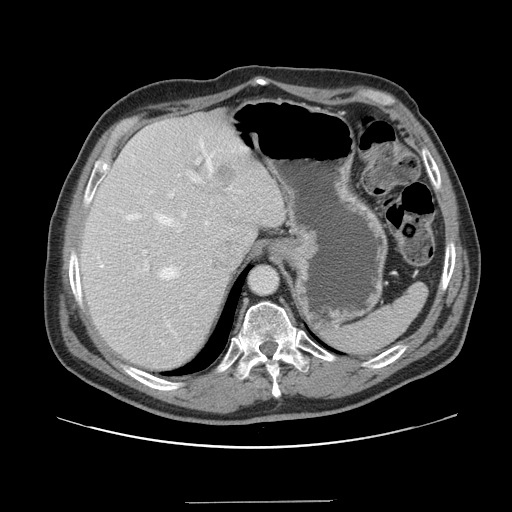
Contrast-enhanced abdominal CT, one axial slice; position 116 of 151 along the scan axis; 120 kVp; intravenous contrast given; soft-tissue window (W 400 / L 40 HU); 2.5 mm slice thickness; 512 × 512 image matrix. Male patient, age 63 years. Case-level facts recorded for this patient, not image findings: diagnosis: colorectal cancer liver metastases, imaged before liver resection; multiple liver metastases: no; largest metastasis: 2.1 cm; chemotherapy before resection: no.
Structures marked on this image (outlined manually by an expert reader):
- hepatic veins: bounding box [x1, y1, x2, y2] px = [100, 139, 213, 279]
- liver: [79, 111, 285, 372]
- planned liver remnant (the part of the liver to remain after resection): [79, 118, 260, 372]
- portal vein (with intrahepatic branches): [143, 157, 232, 271]
- liver metastasis: [217, 165, 236, 184]